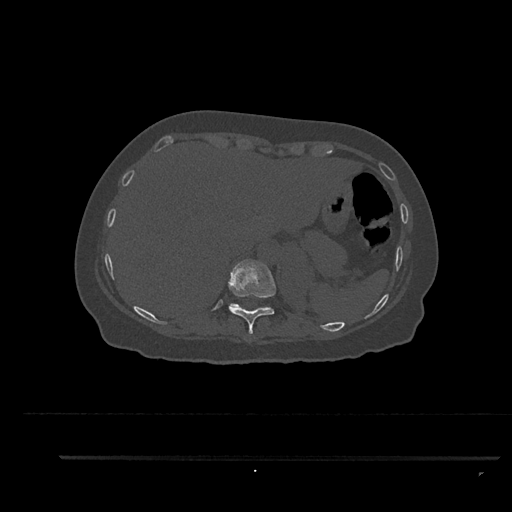
CT including the spine, one axial slice; position 354 of 797 along the scan axis; reconstruction kernel Br40s/3; bone window (W 1800 / L 400 HU); 512 × 512 image matrix, field of view 408 × 408 mm. Patient: female, 44 years. Case-level facts recorded for this patient, not image findings: primary cancer: renal.
Outlined on this slice (semi-automatically segmented with operator editing):
- T10 vertebra: box from (x=228, y=259) to (x=276, y=334) px
- T11 vertebra: (x=230, y=303)–(x=238, y=305)